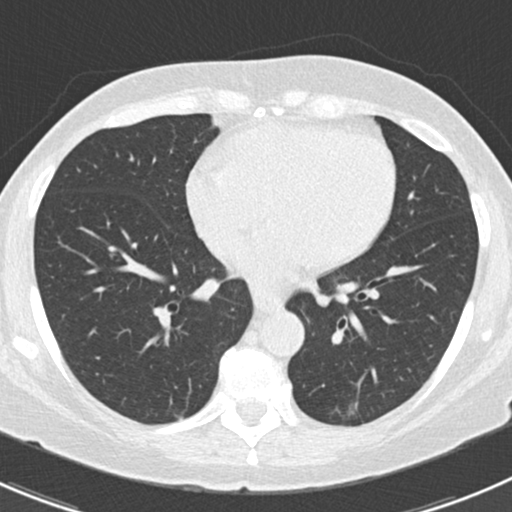
Chest CT (low-dose screening protocol), one axial image; second annual screen; lung window (W 1500 / L -600 HU); 2 mm slice thickness. Female, age 64 years at enrolment. Former smoker at enrolment.
- Expert-annotated lung lesion, box from (x=331, y=395) to (x=378, y=431) px.
- Reader record for this screening exam (exam-level; its link to the box is not recorded): non-calcified nodule or mass ≥4 mm, left lower lobe, 8 × 3 mm, poorly defined margins, soft tissue attenuation, pre-existing on the prior screen: yes; interval growth: no.
- Official screen result: positive, no significant change: stable abnormalities potentially related to lung cancer, unchanged since the prior screening exam.
- Lung cancer was diagnosed 101 days after this screen: adenocarcinoma, NOS, left lower lobe, poorly differentiated (G3), stage IA (AJCC 6th edition), 8 mm at pathology.